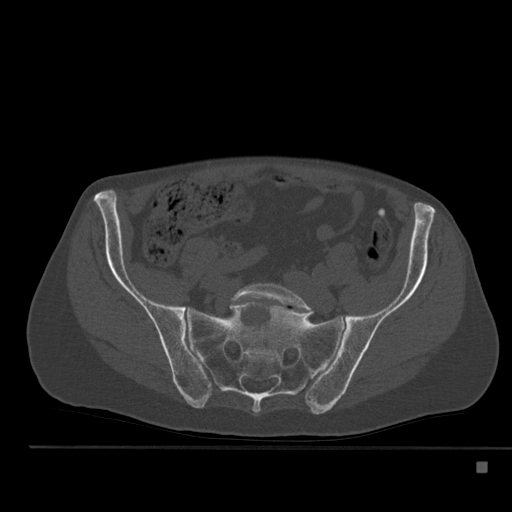
CT including the spine, one axial slice. Slice 101 of 517 in the series (ordered by position). Reconstruction kernel Br40s. Bone window (W 1800 / L 400 HU). 1.5 mm slice thickness. 512 × 512 image matrix. Patient: male, 70 years. From the clinical record (not read from this slice): primary cancer: renal; vertebrae with lytic lesions (as recorded): T4, T6, T10, T12, L3, L4, L5.
Structures marked on this image (semi-automatically segmented with operator editing):
- L5 vertebra: bounding box <231,283,314,312> (left, top, right, bottom; pixels)